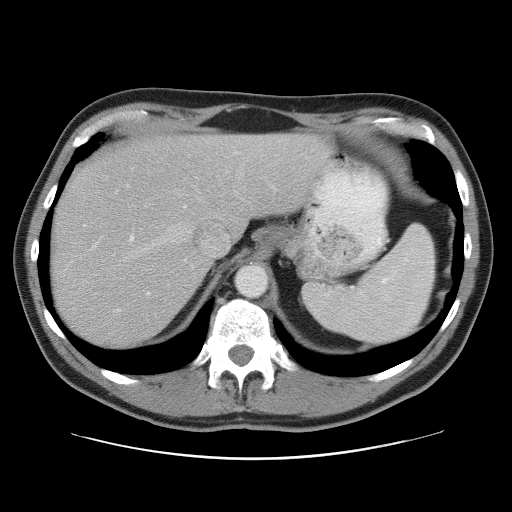
Contrast-enhanced abdominal CT, one axial slice; reconstruction kernel STANDARD; 120 kVp; intravenous contrast given; soft-tissue window (W 400 / L 40 HU); 5 mm slice thickness; 512 × 512 image matrix, field of view 393 × 393 mm. Male patient, age 70 years. Case-level facts recorded for this patient, not image findings: diagnosis: colorectal cancer liver metastases, imaged before liver resection; multiple liver metastases: yes; largest metastasis: 4 cm.
Structures marked on this image (expert manual segmentation):
- hepatic veins: bounding box [x1, y1, x2, y2] px = [137, 171, 243, 297]
- liver: [50, 134, 322, 349]
- planned liver remnant (the part of the liver to remain after resection): [112, 135, 323, 222]
- portal vein (with intrahepatic branches): [129, 235, 134, 241]